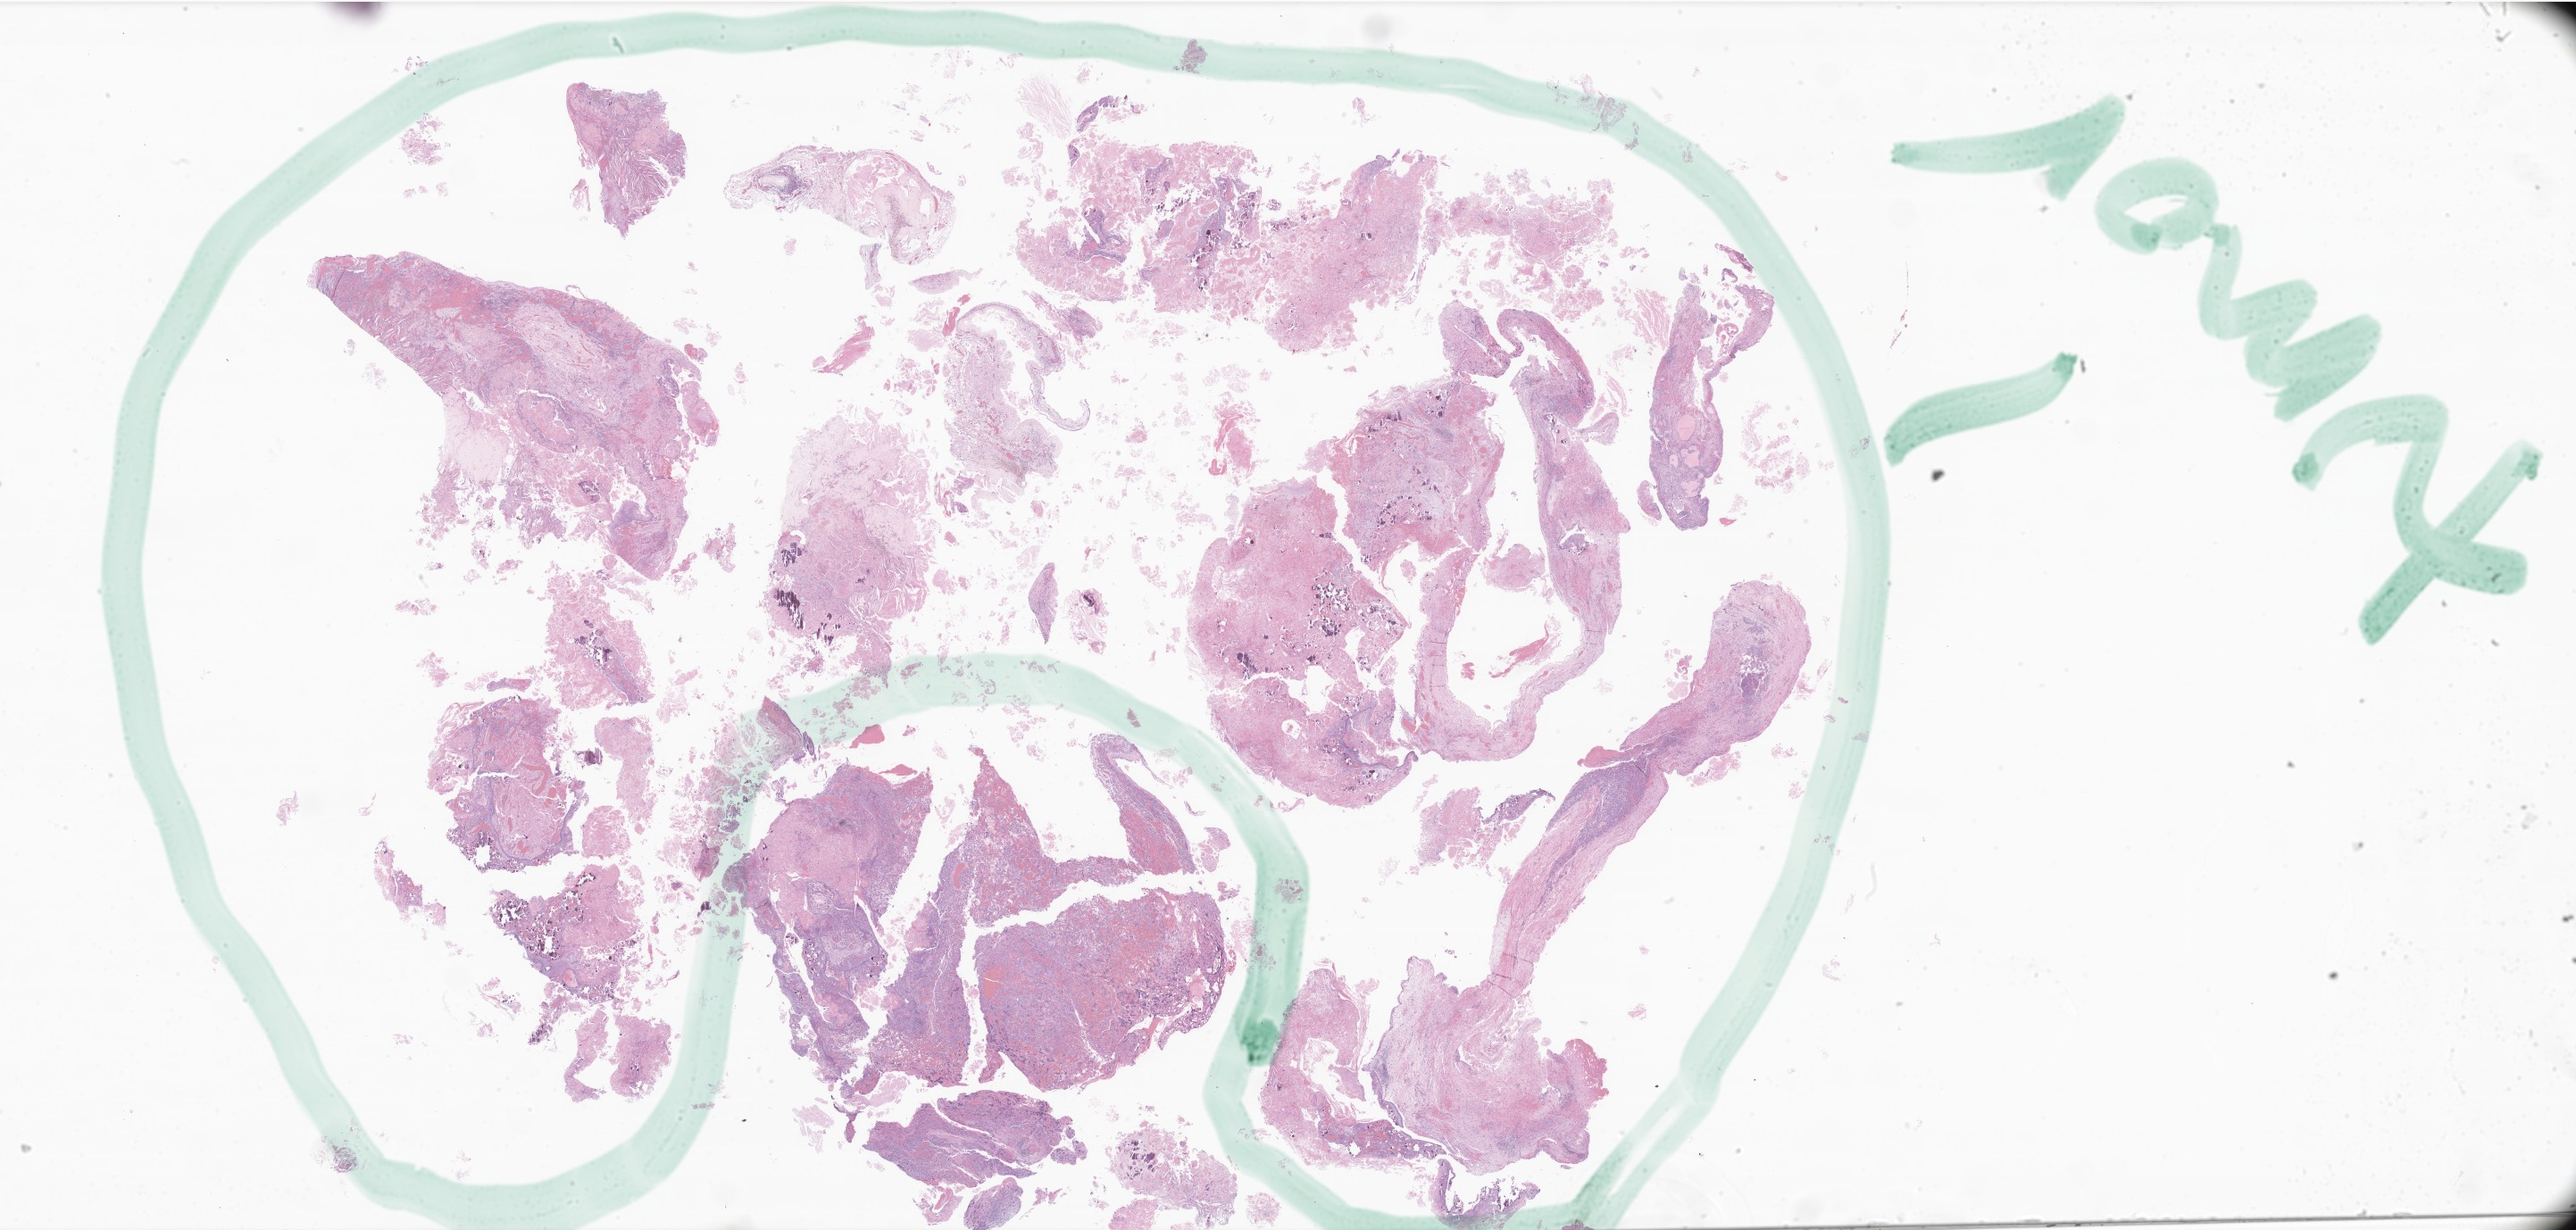
Whole-slide image, H&E stain of tumor tissue from the brain, whole scanned area (about 48.7 x 23.2 mm) shown as a low-resolution overview, formalin-fixed, paraffin-embedded (FFPE) tissue. Male patient, age 146 months (12 years 2 months).
Diagnosis: Craniopharyngioma, adamantinomatous.